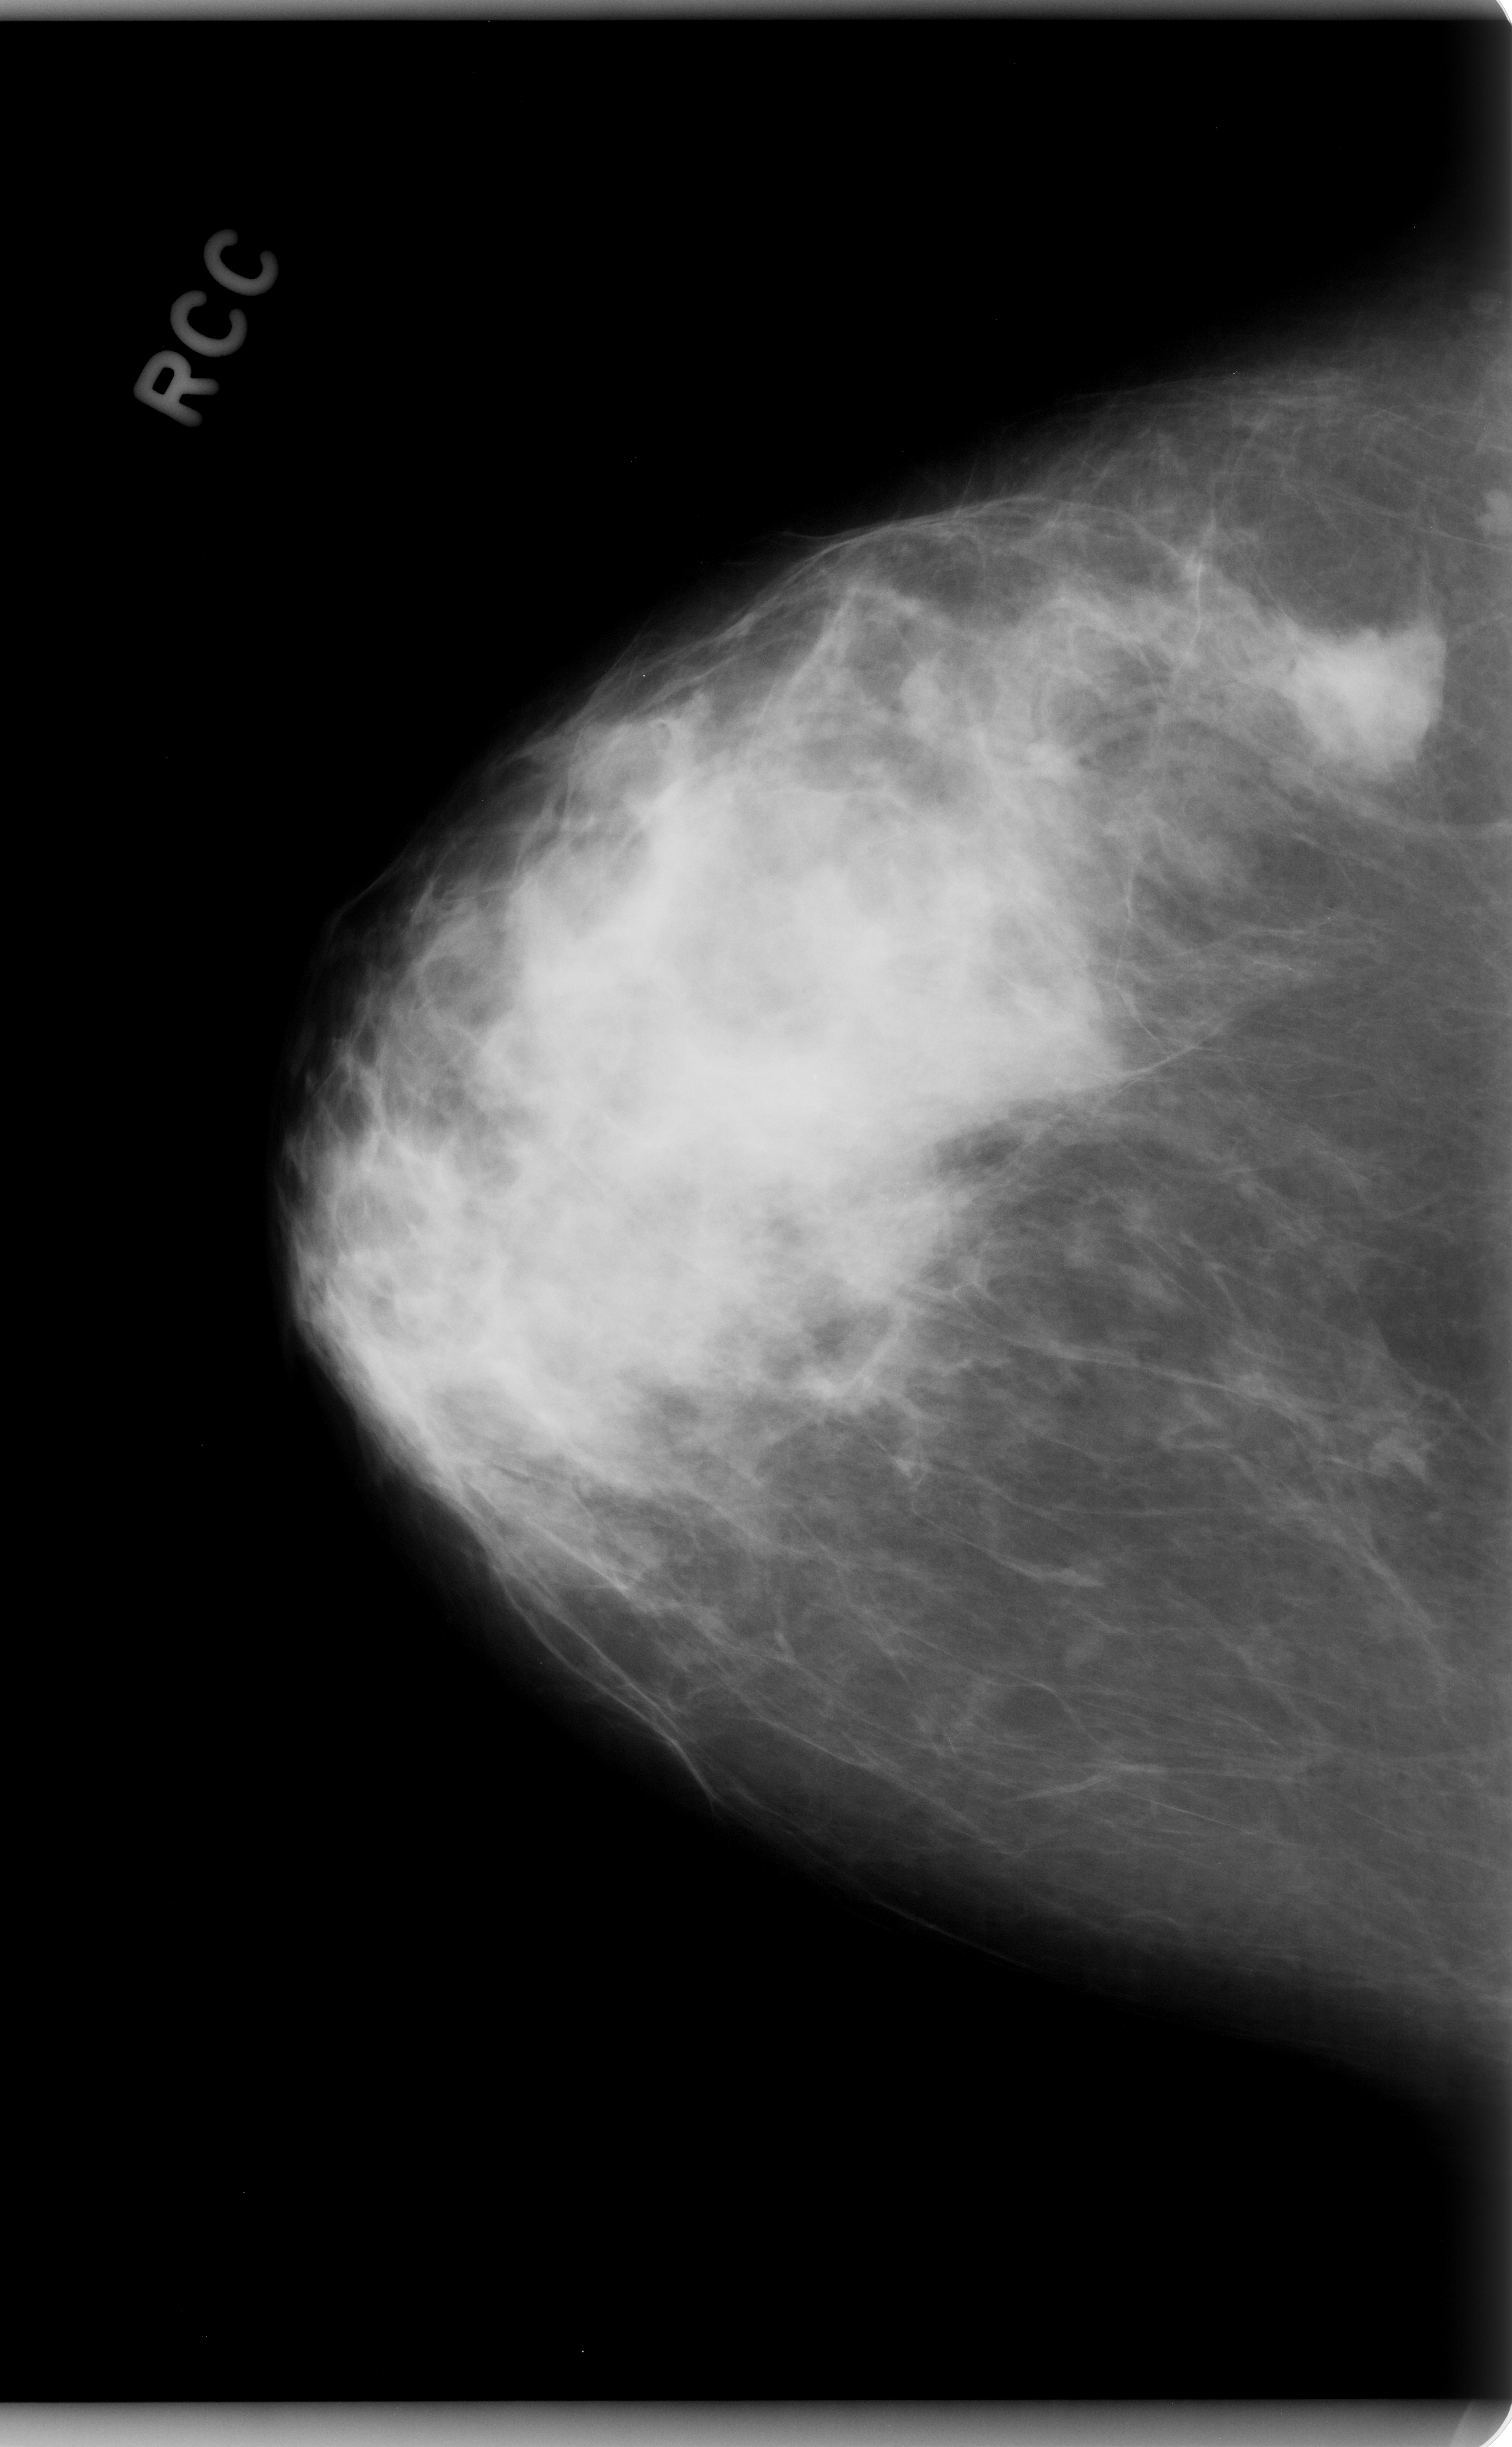
Mammogram (digitized film); right breast; craniocaudal (CC) view; breast composition: heterogeneously dense (BI-RADS density category 3 of 4).
Mass, shape irregular, margins microlobulated; BI-RADS assessment category 5; pathology result (as recorded, not read from the image): malignant.